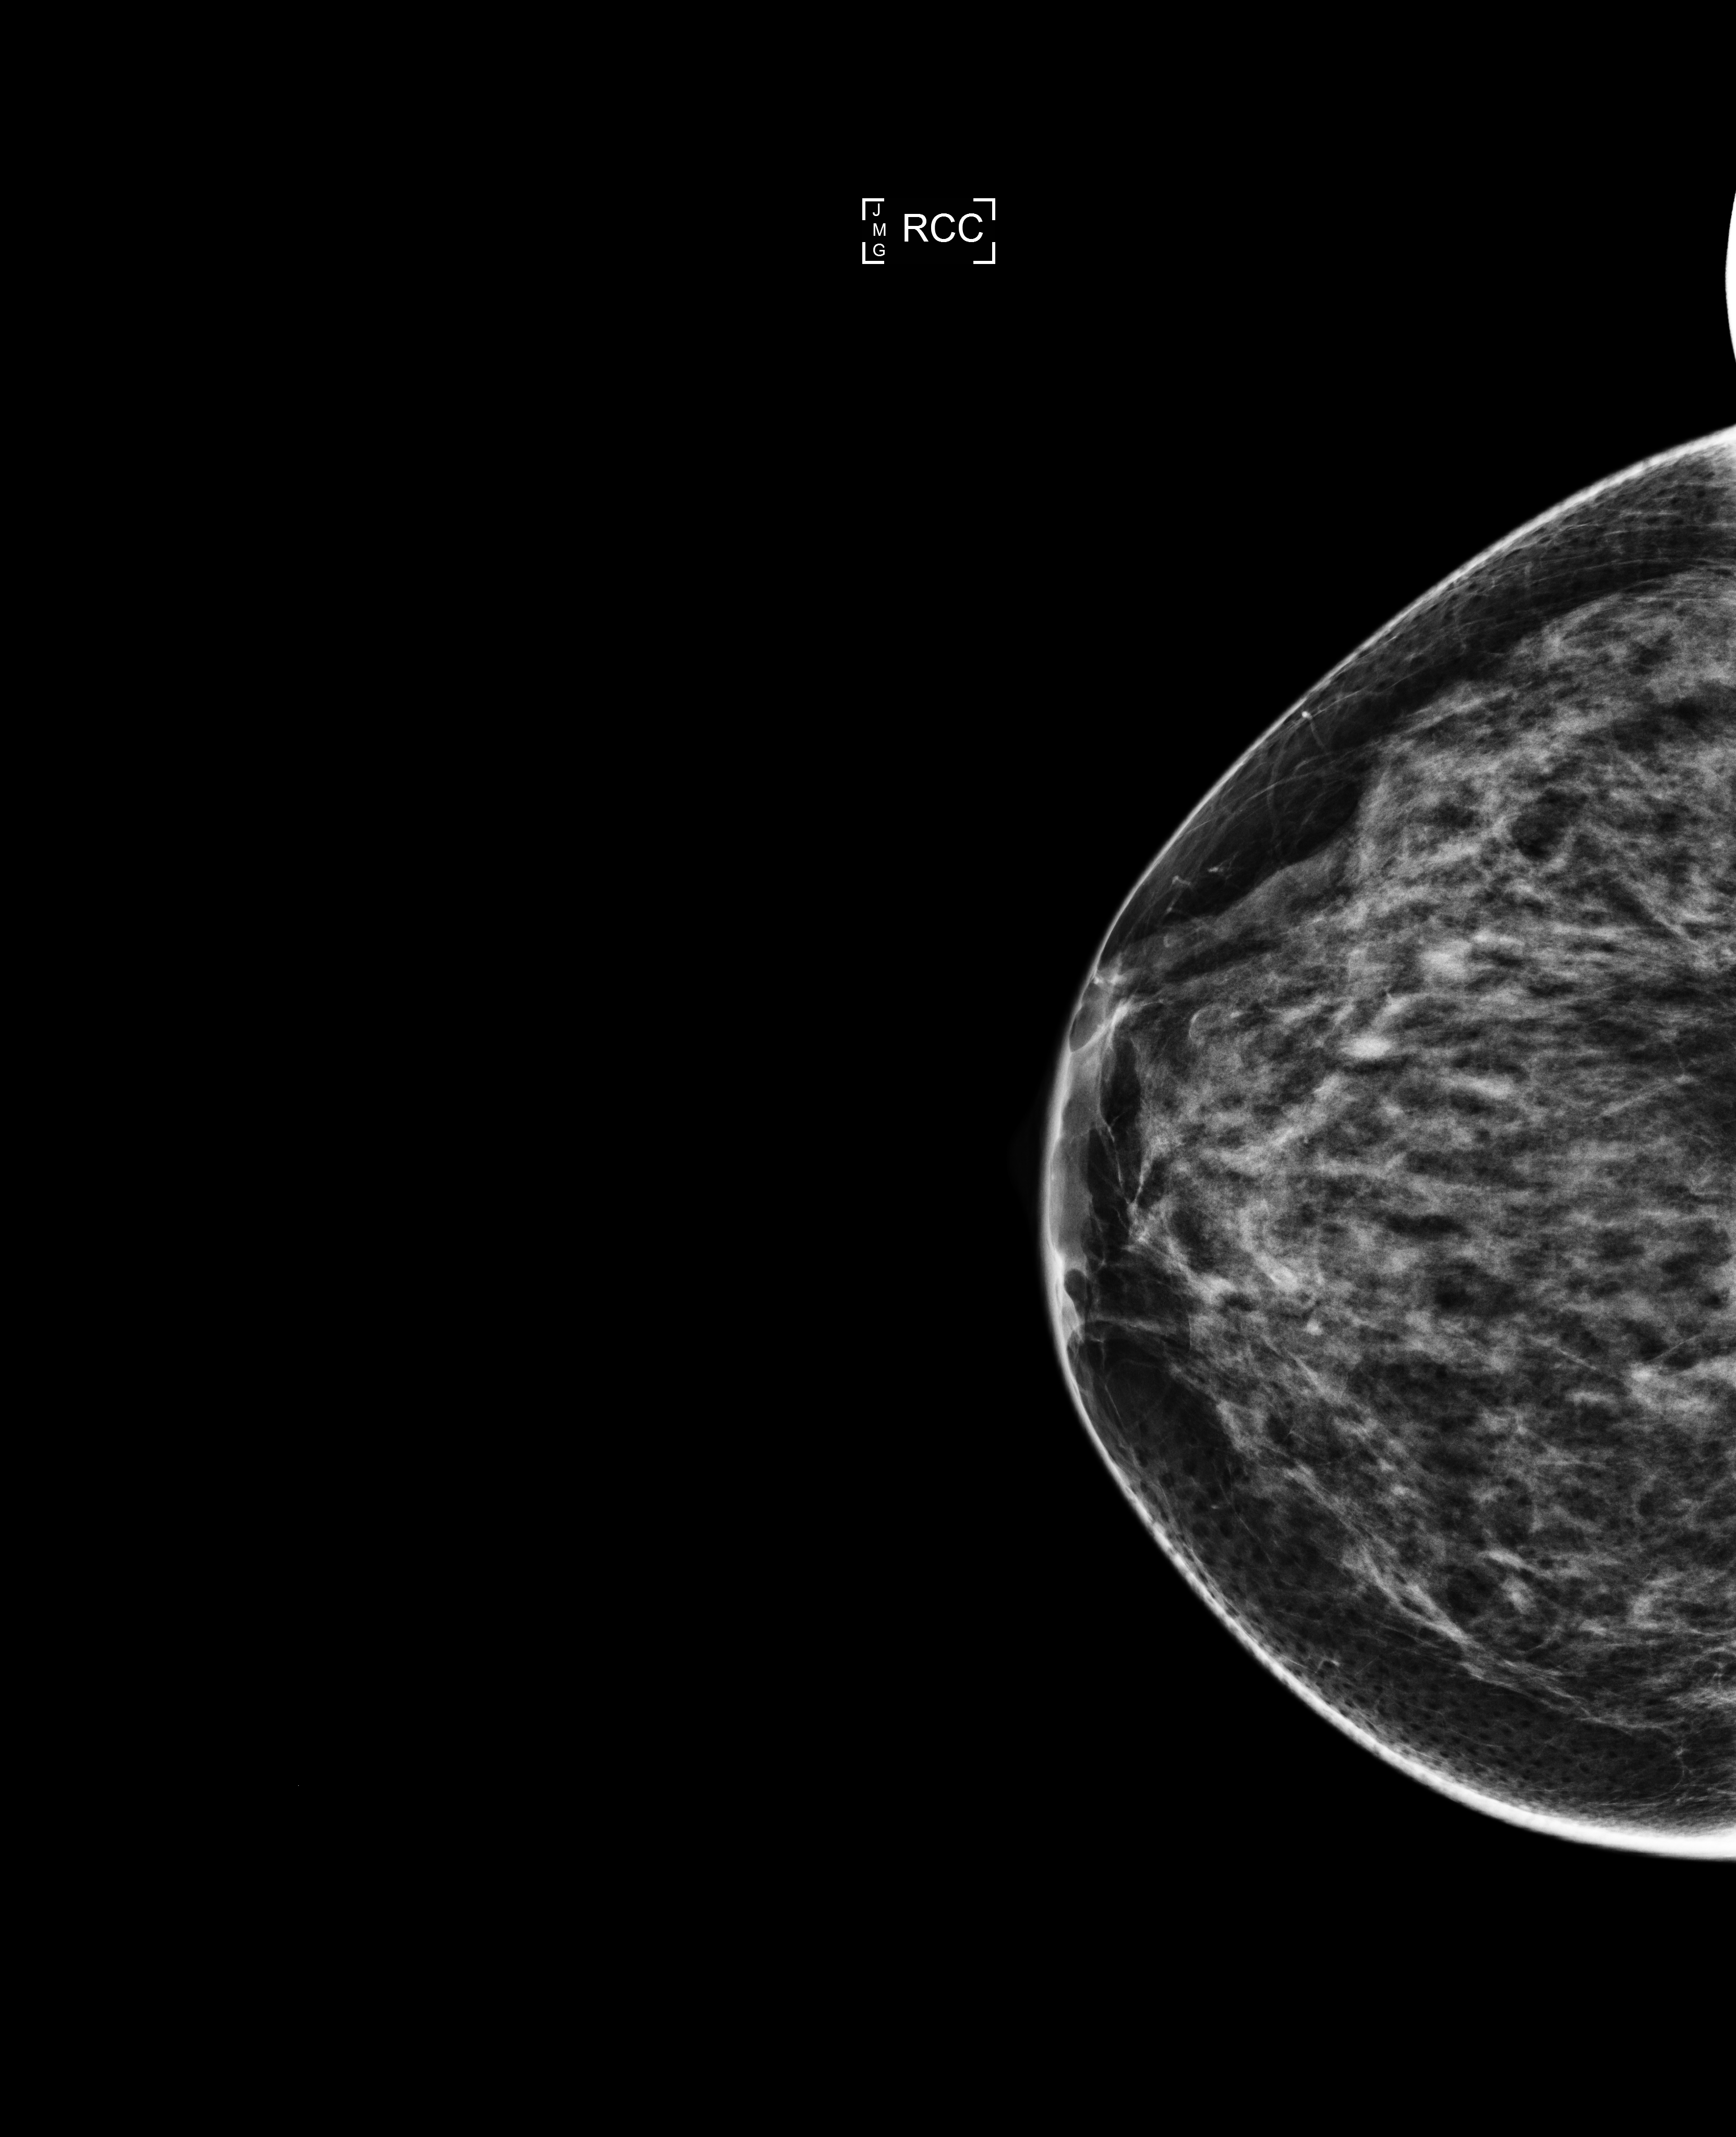
Digital mammogram (FFDM), right breast, craniocaudal (CC) view, annual screening mammography examination, system: Selenia Dimensions. Patient: female, 55 years.
- breast density at the screening exam (both breasts): heterogeneously dense (BI-RADS density category c)
- final BI-RADS category for the screening round (tomosynthesis exam, both breasts): category 1
- recall: no recall after this screen